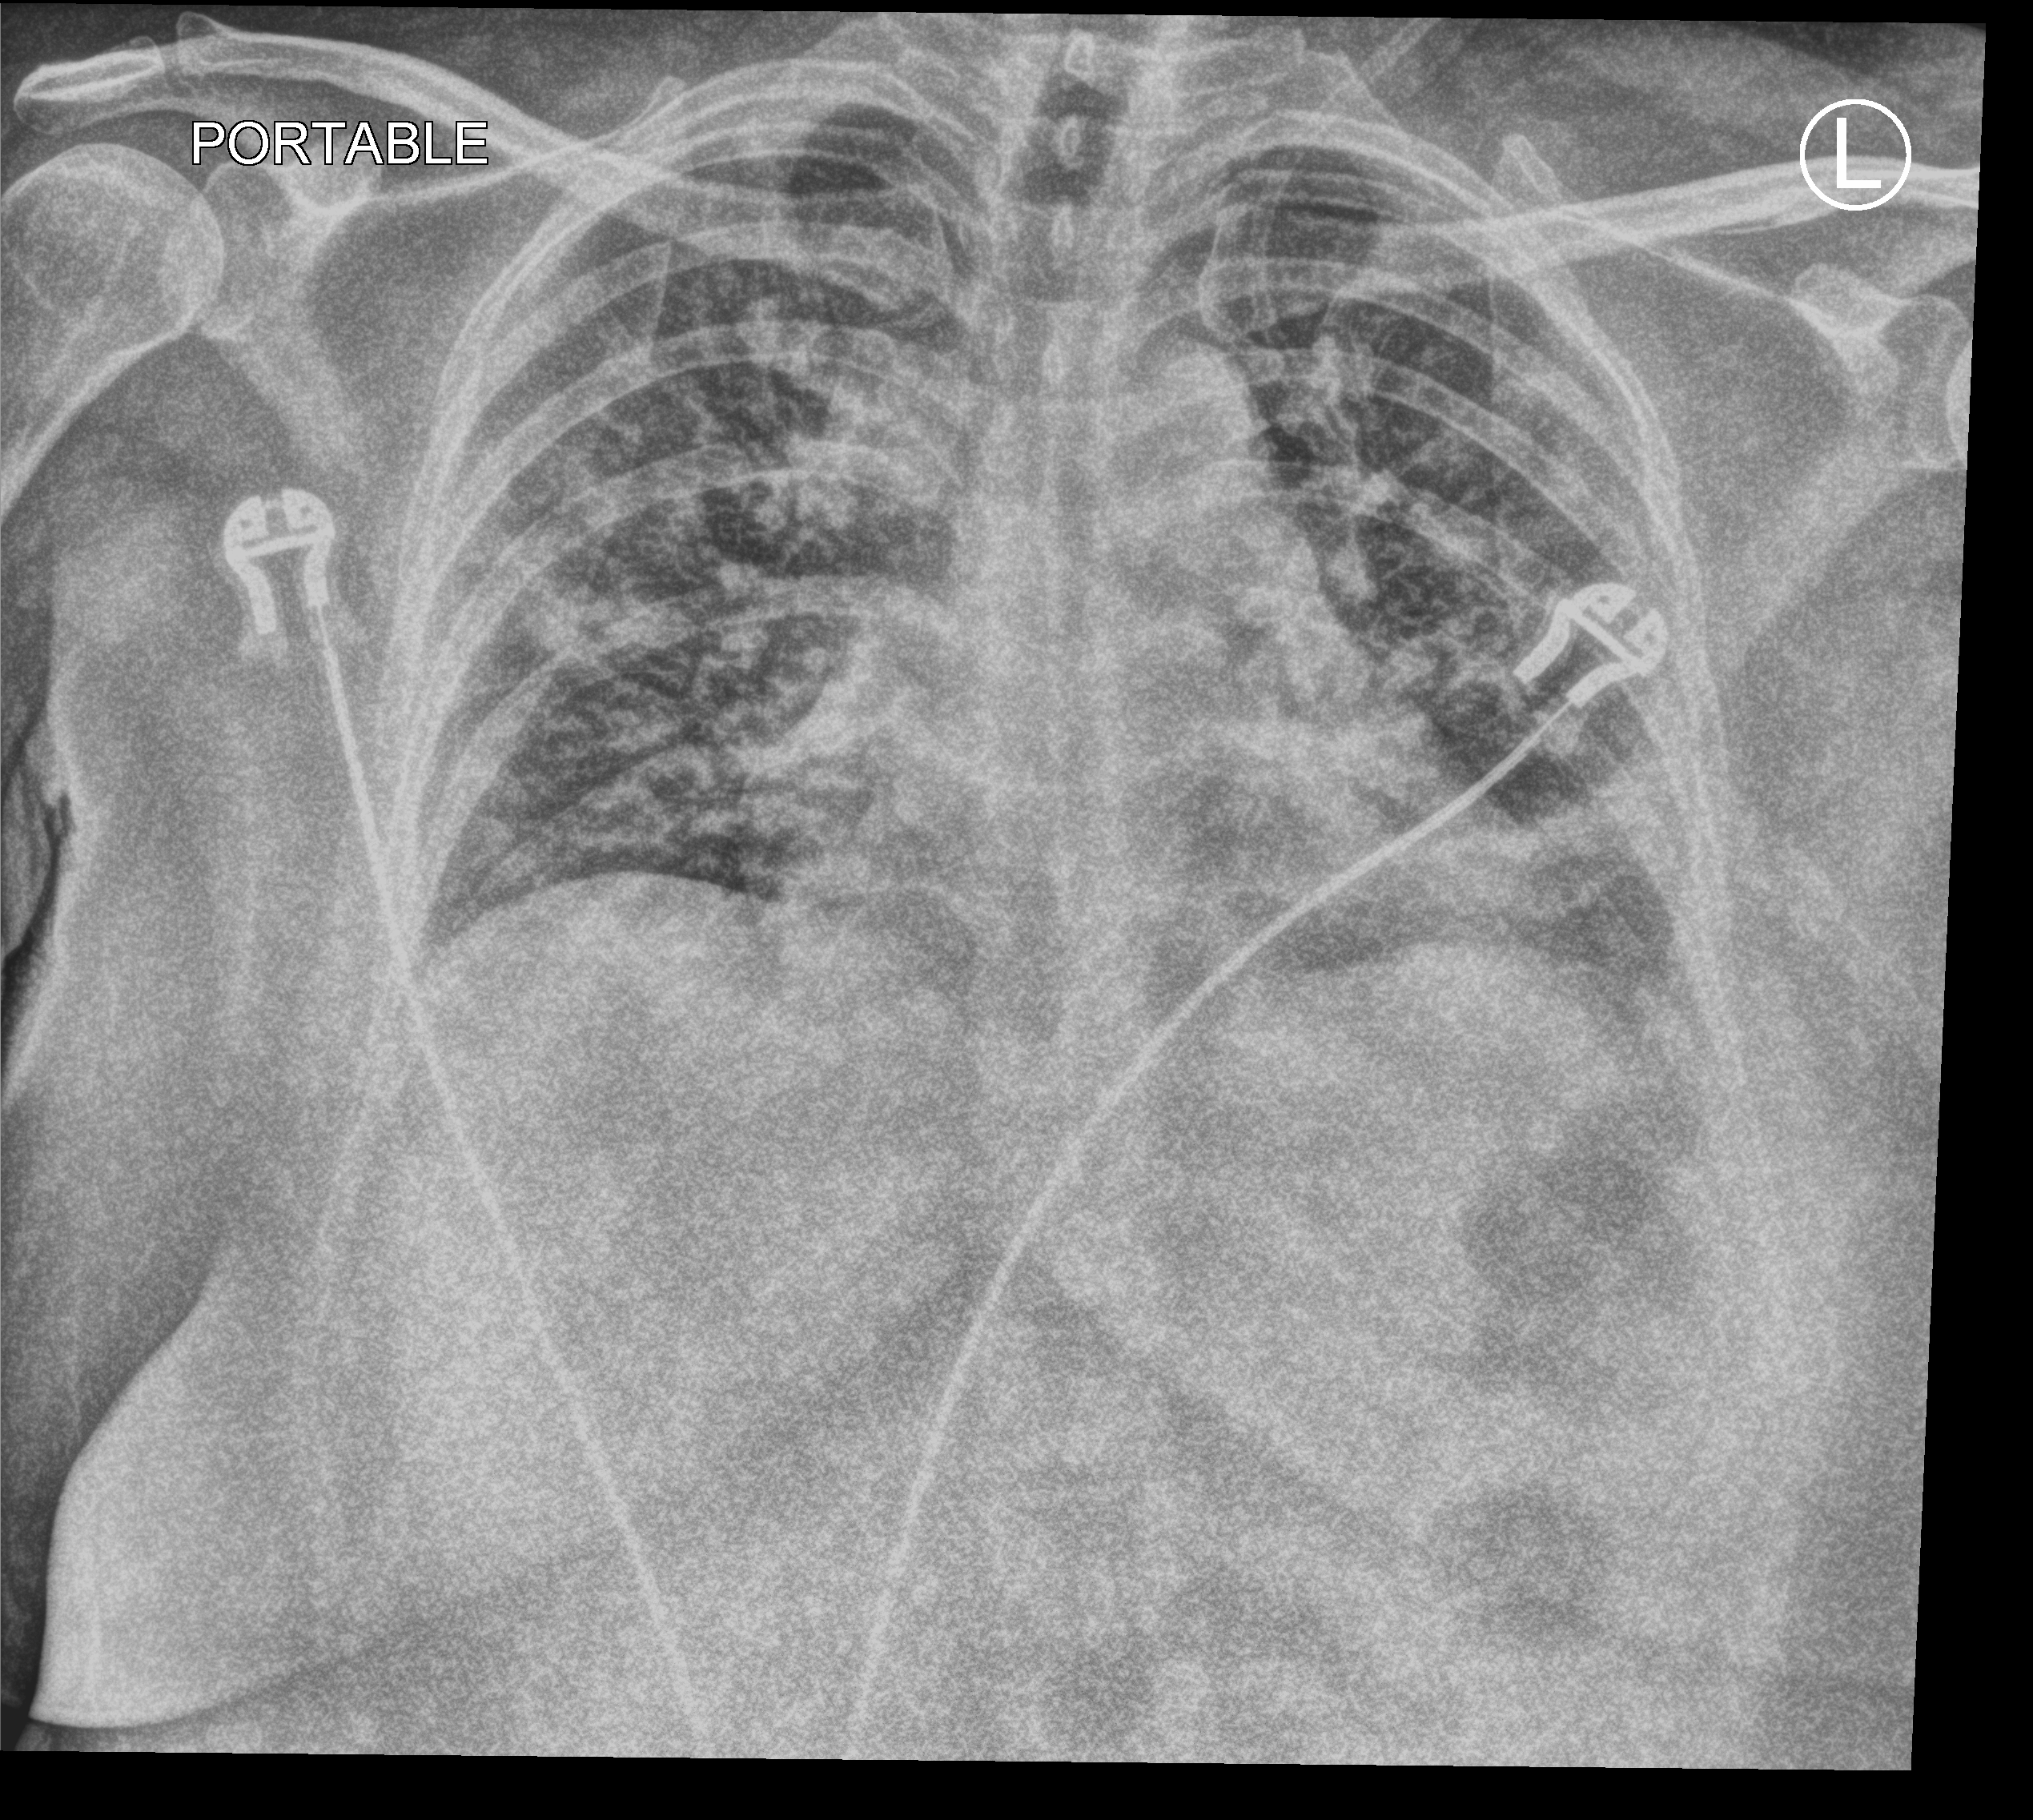
Portable chest radiograph; anteroposterior (AP) projection. Adult patient hospitalised with COVID-19, age 18–59 years.
Hospital-stay facts (about this admission, not read from this image; timing relative to this image not recorded): admitted to intensive care during this hospital stay: yes; smoking status (admission record): never.